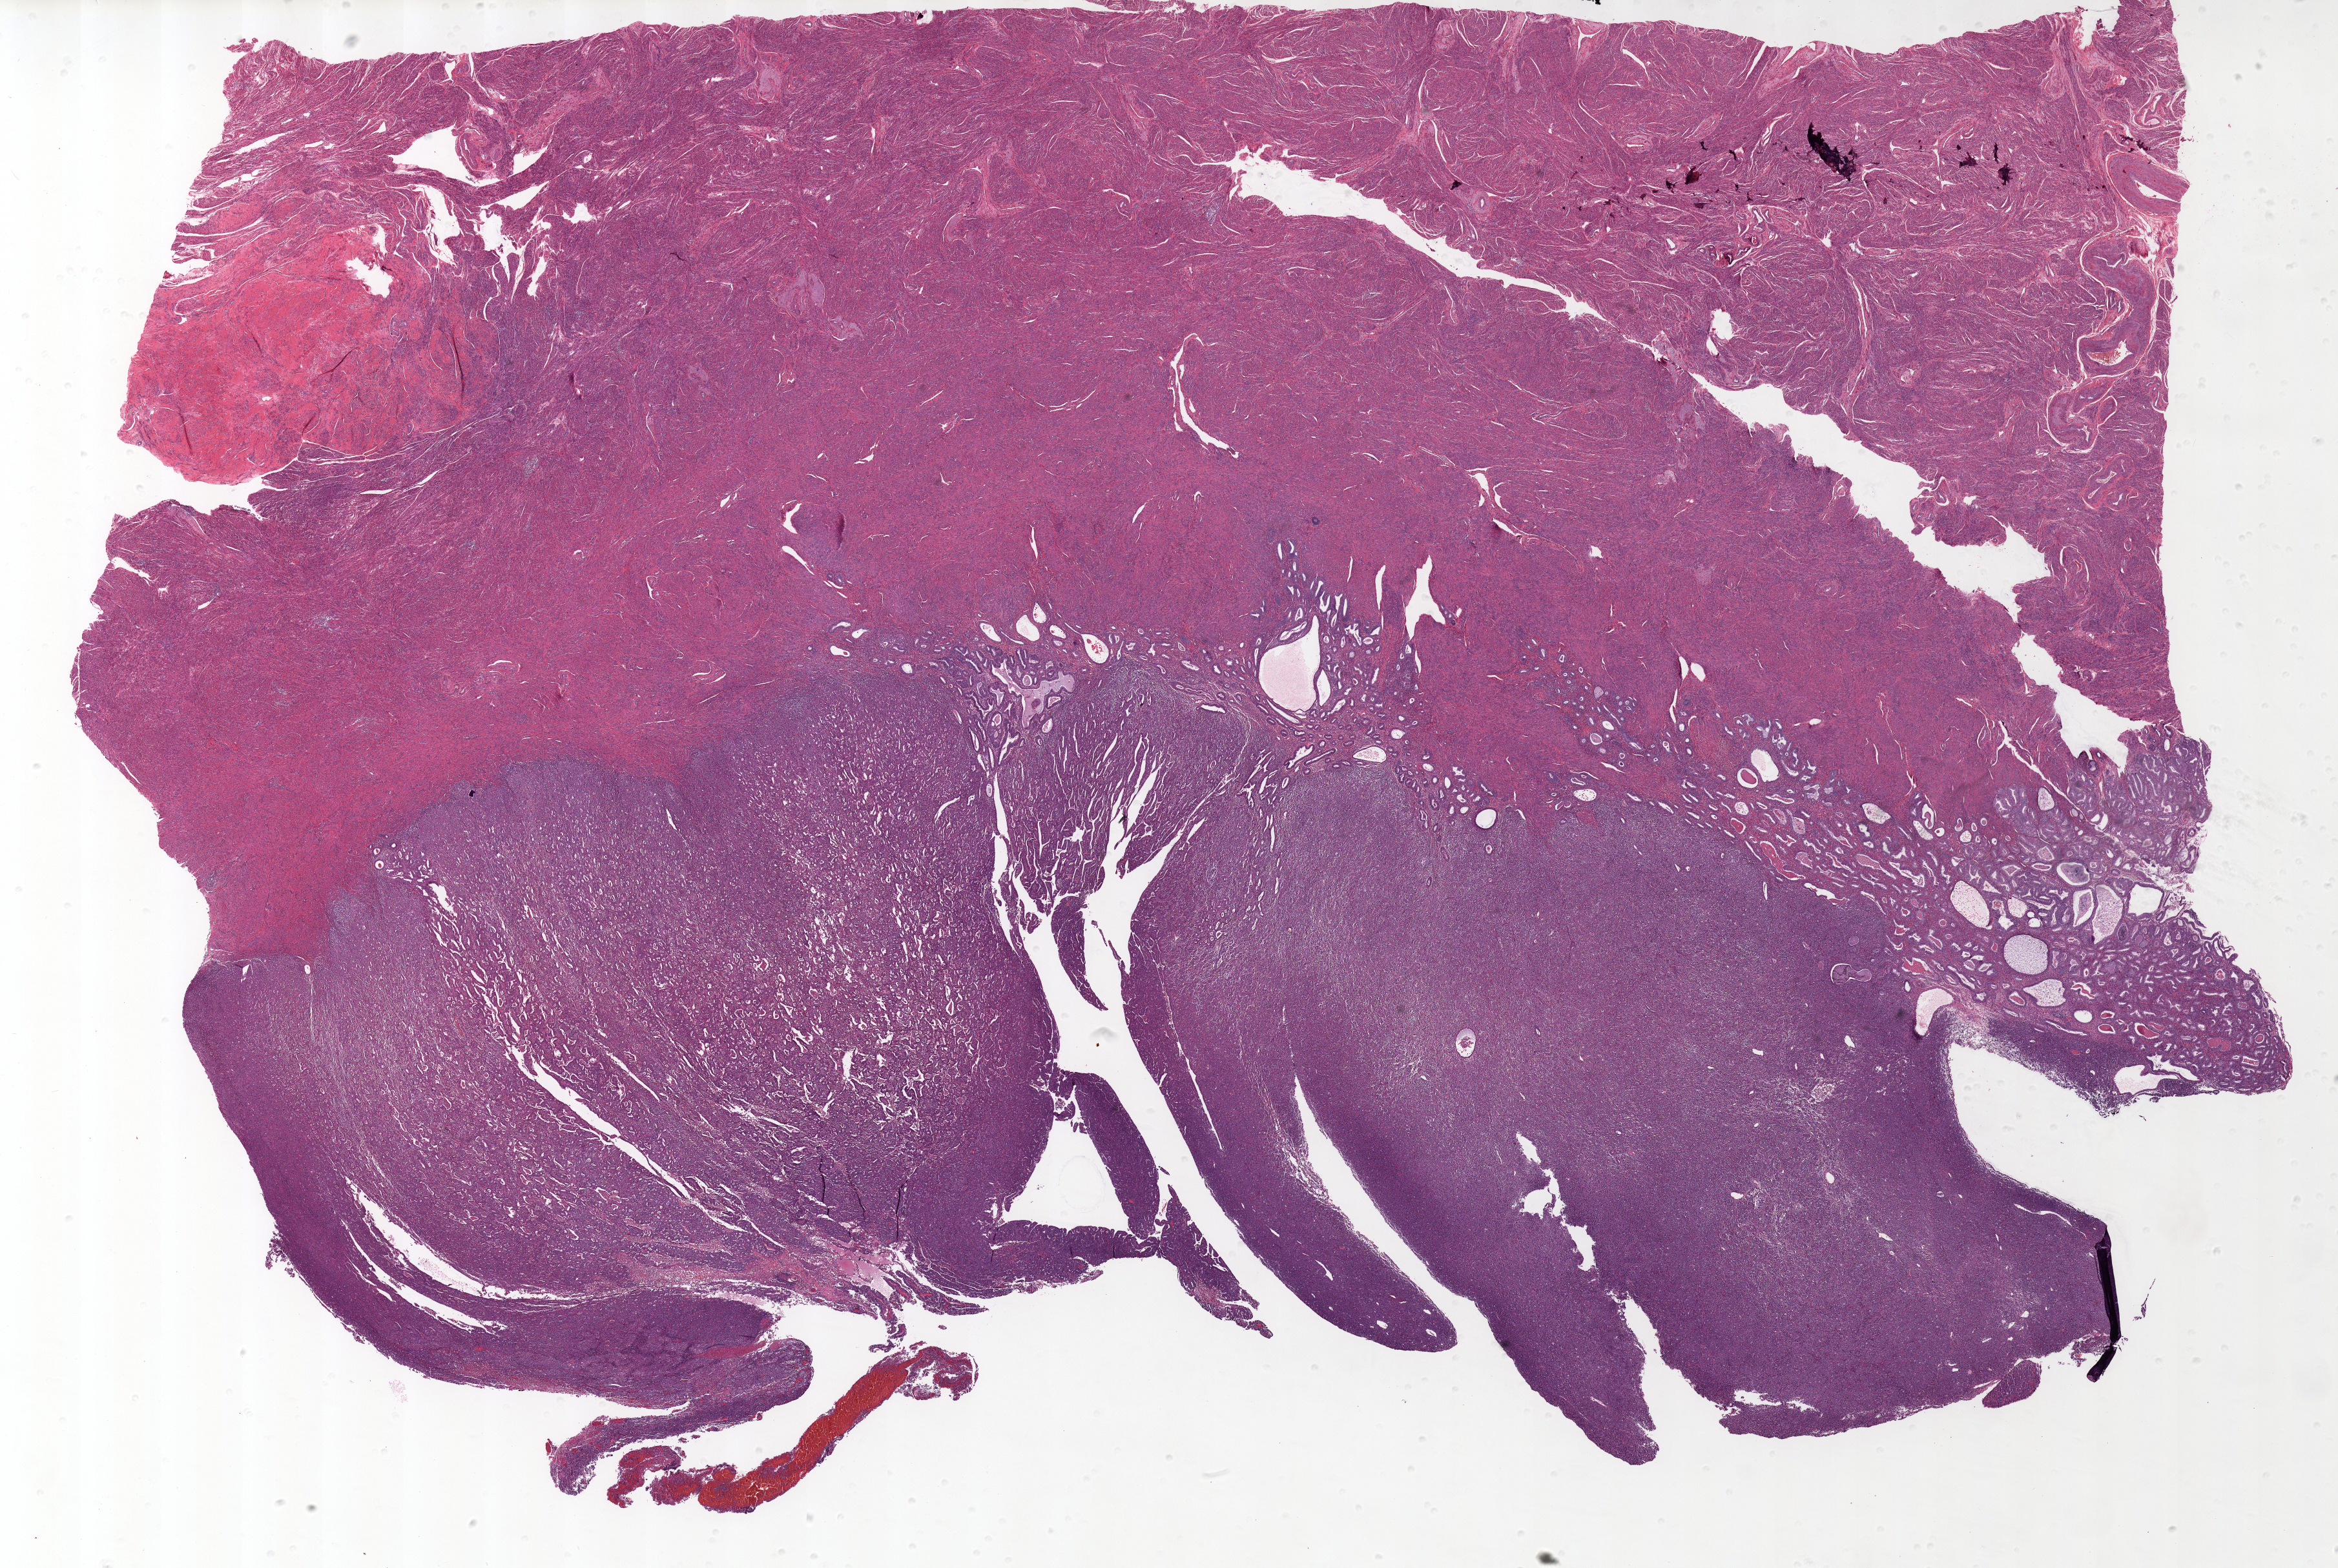
Digitized Hematoxylin and eosin (H&E) stained tissue section (whole slide), a low-resolution overview of the entire scanned area, about 28.8 x 19.3 mm (slide scanned at 20x); formalin-fixed paraffin-embedded (FFPE) diagnostic section; sample: primary tumour, uterus. Female, age 69 years at initial diagnosis. Histologic grade: G3 (poorly differentiated).
Diagnosis: Endometrioid adenocarcinoma, NOS (endometrium). FIGO stage: IA. Lymph nodes positive (case pathology): 0 of 13 examined.